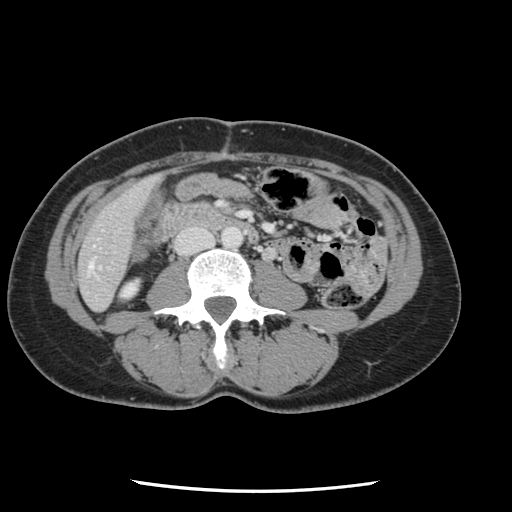
Contrast-enhanced abdominal CT, one axial slice; position 17 of 134 along the scan axis; 120 kVp; intravenous contrast given; soft-tissue window (W 400 / L 40 HU); 2.5 mm slice thickness; 512 × 512 image matrix, field of view 330 × 330 mm. Female patient, age 43 years. From the clinical record (not read from this slice): diagnosis: colorectal cancer liver metastases, imaged before liver resection.
Annotated regions visible in this slice (manually delineated by an expert):
- hepatic veins: bounding box (x1, y1, x2, y2) in pixels: (89, 263, 93, 270)
- liver: (80, 178, 156, 310)
- planned liver remnant (the part of the liver to remain after resection): (80, 178, 156, 310)